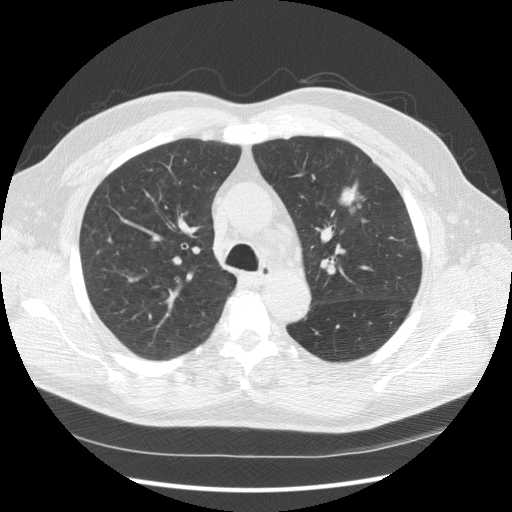
Low-dose screening chest CT, one axial slice; position 108 of 157 along the scan axis; lung window (W 1500 / L -600 HU); 512 × 512 image matrix.
Outlined on this slice (manually delineated by an expert):
- lesion 1 (tumor, upper lobe of left lung): bounding box [x1, y1, x2, y2] px = [340, 184, 364, 215]